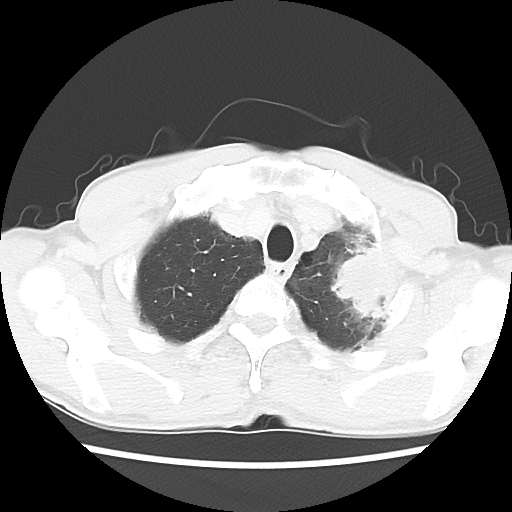
Chest CT, one axial slice; slice 52 of 60 in the series (ordered by position); reconstruction kernel LUNG; 120 kVp; lung window (W 1500 / L -600 HU); 5 mm slice thickness; 512 × 512 image matrix, field of view 308 × 308 mm. Male patient, age 64 years. Case-level facts recorded for this patient, not image findings: clinical TNM (as recorded): T3 N3 M0.
Annotated regions visible in this slice (rectangle marked by the reading radiologist):
- lung tumour (recorded histology: adenocarcinoma): bounding box (x1, y1, x2, y2) in pixels: (325, 236, 401, 330)